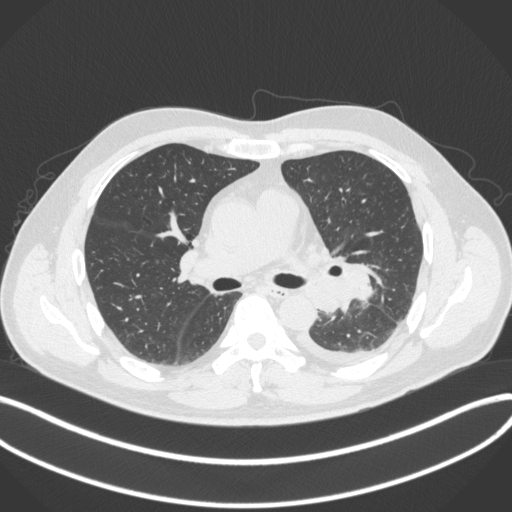
Chest CT, one axial slice. Position 214 of 350 along the scan axis. Reconstruction kernel B31f. 120 kVp. Lung window (W 1500 / L -600 HU). 1 mm slice thickness. 512 × 512 image matrix. Patient: male, 58 years. From the clinical record (not read from this slice): clinical TNM (as recorded): T3 N1 M1b.
Outlined on this slice (rectangle marked by the reading radiologist):
- lung tumour (recorded histology: small cell carcinoma): bounding box <341,257,379,310> (left, top, right, bottom; pixels)